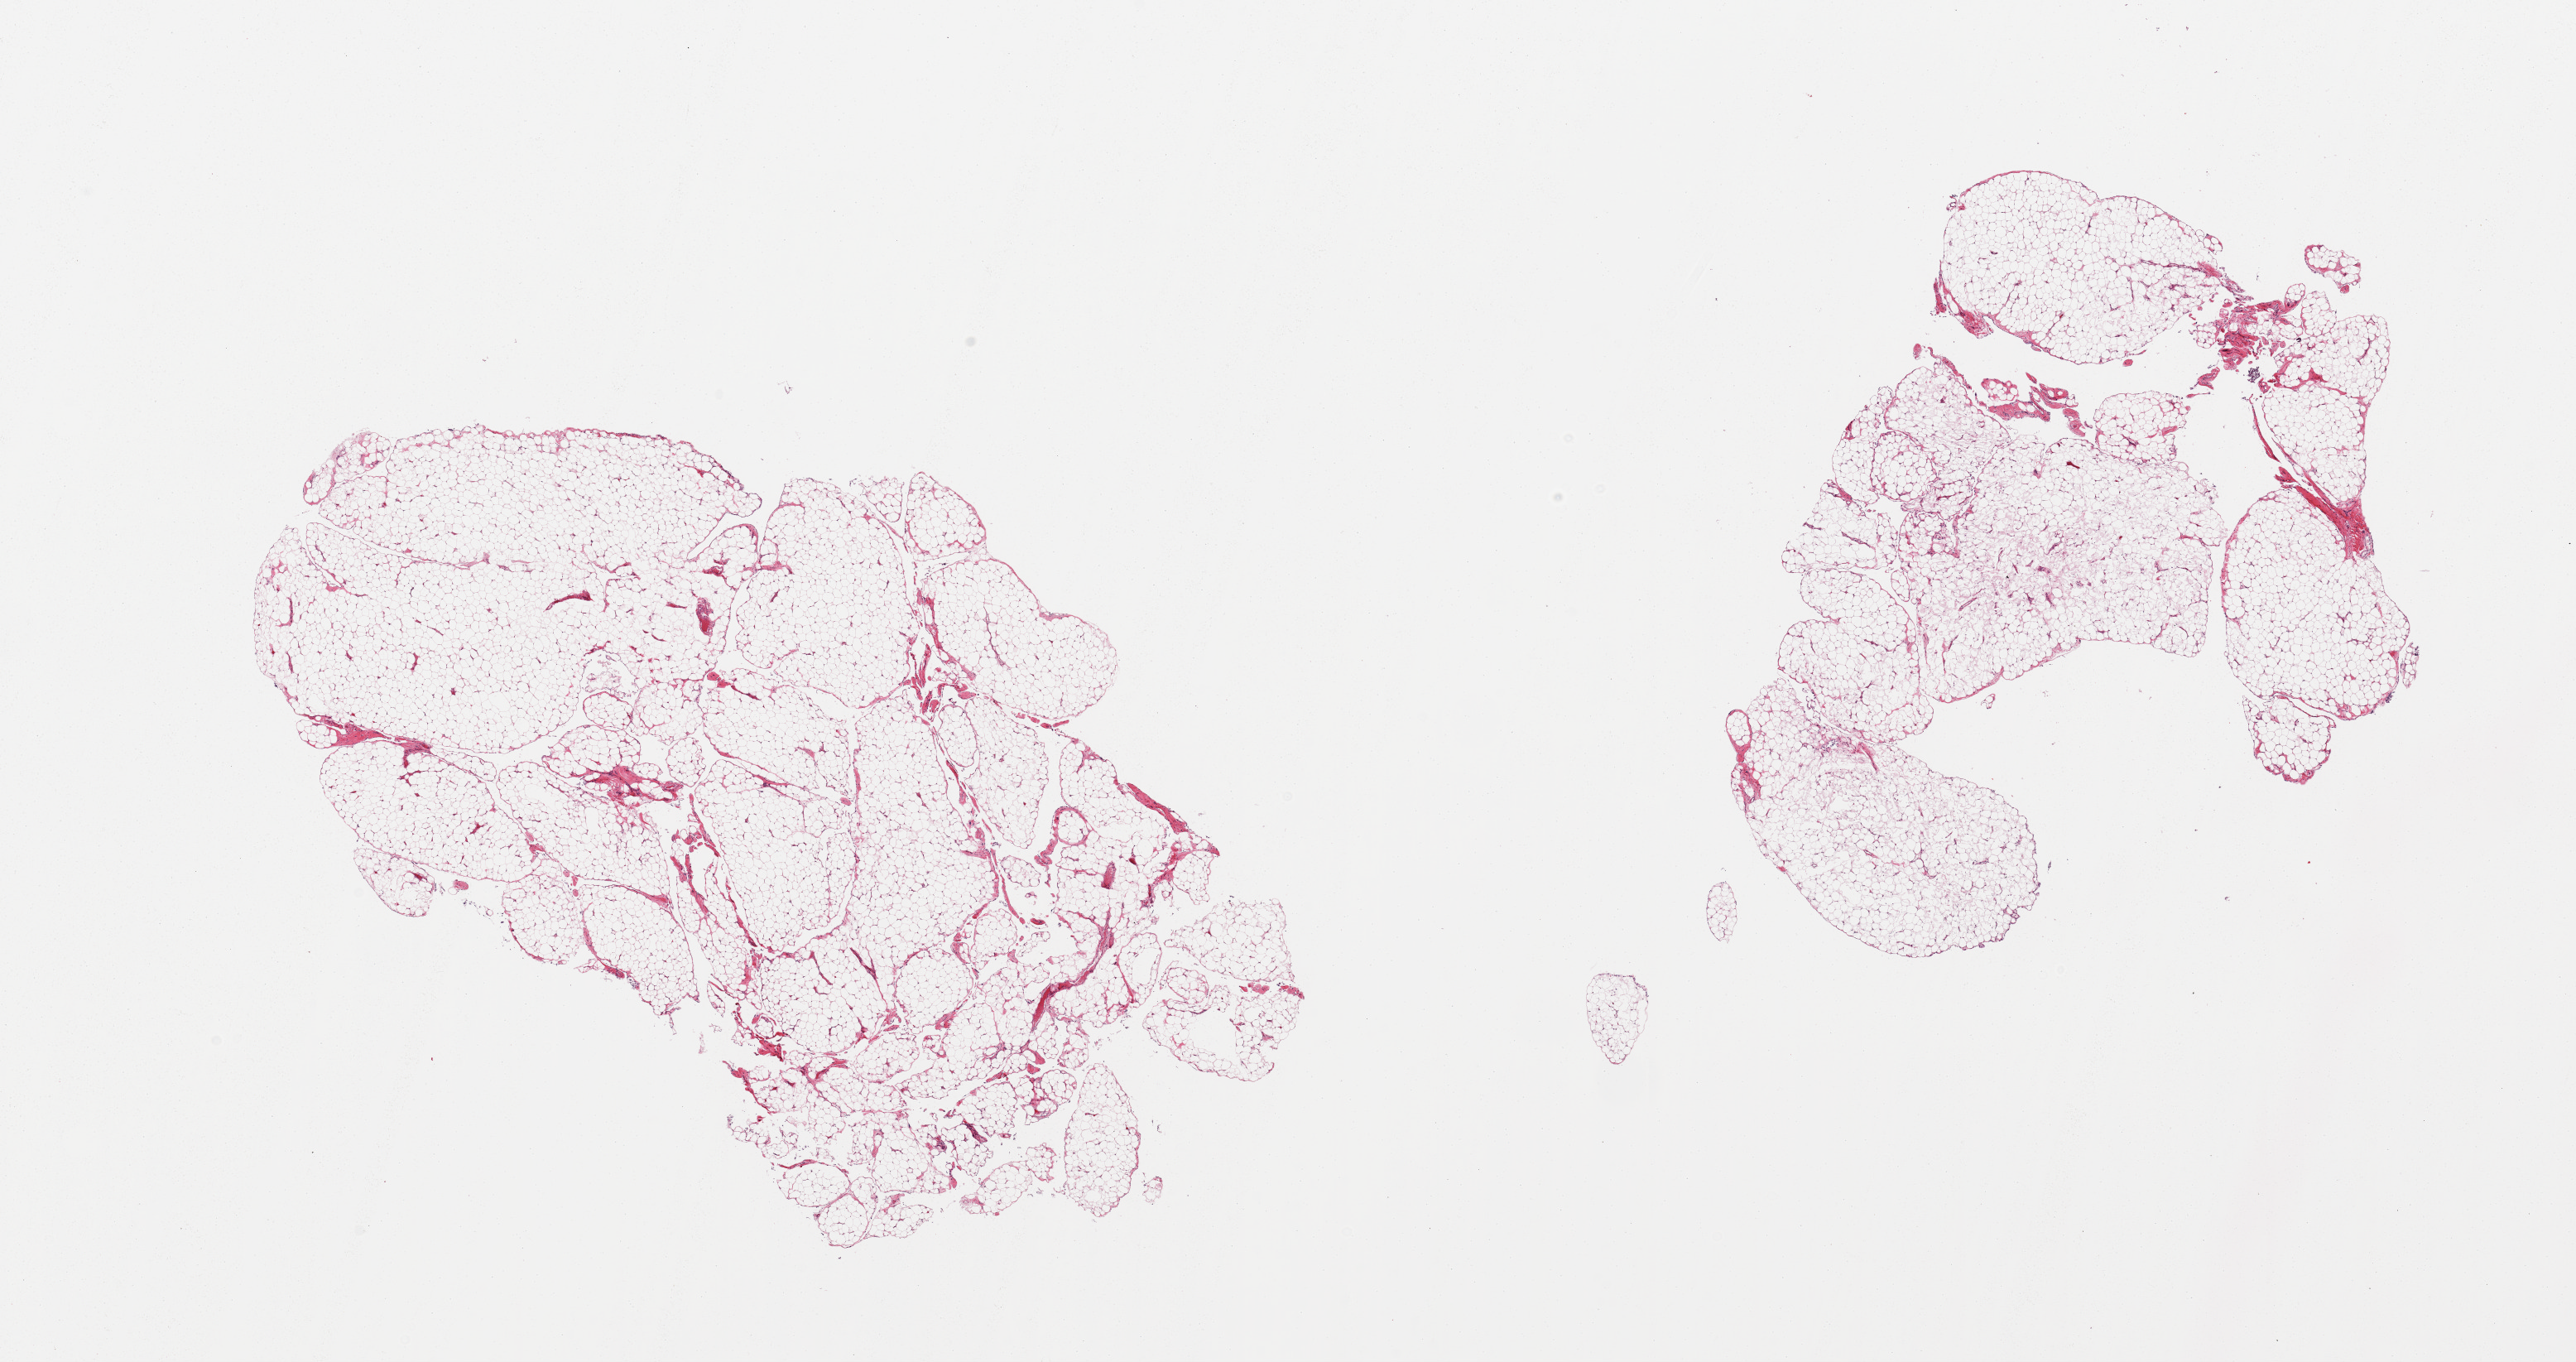
Hematoxylin and eosin (H&E) whole-slide image, brightfield, low-resolution overview of the scanned area, about 24.6 x 13.0 mm, PAXgene-fixed, paraffin-embedded tissue, sampled site (target tissue): omentum, tissue donor sample. Male donor.
Review note (as recorded): 2 pieces; minimal fibrous content.